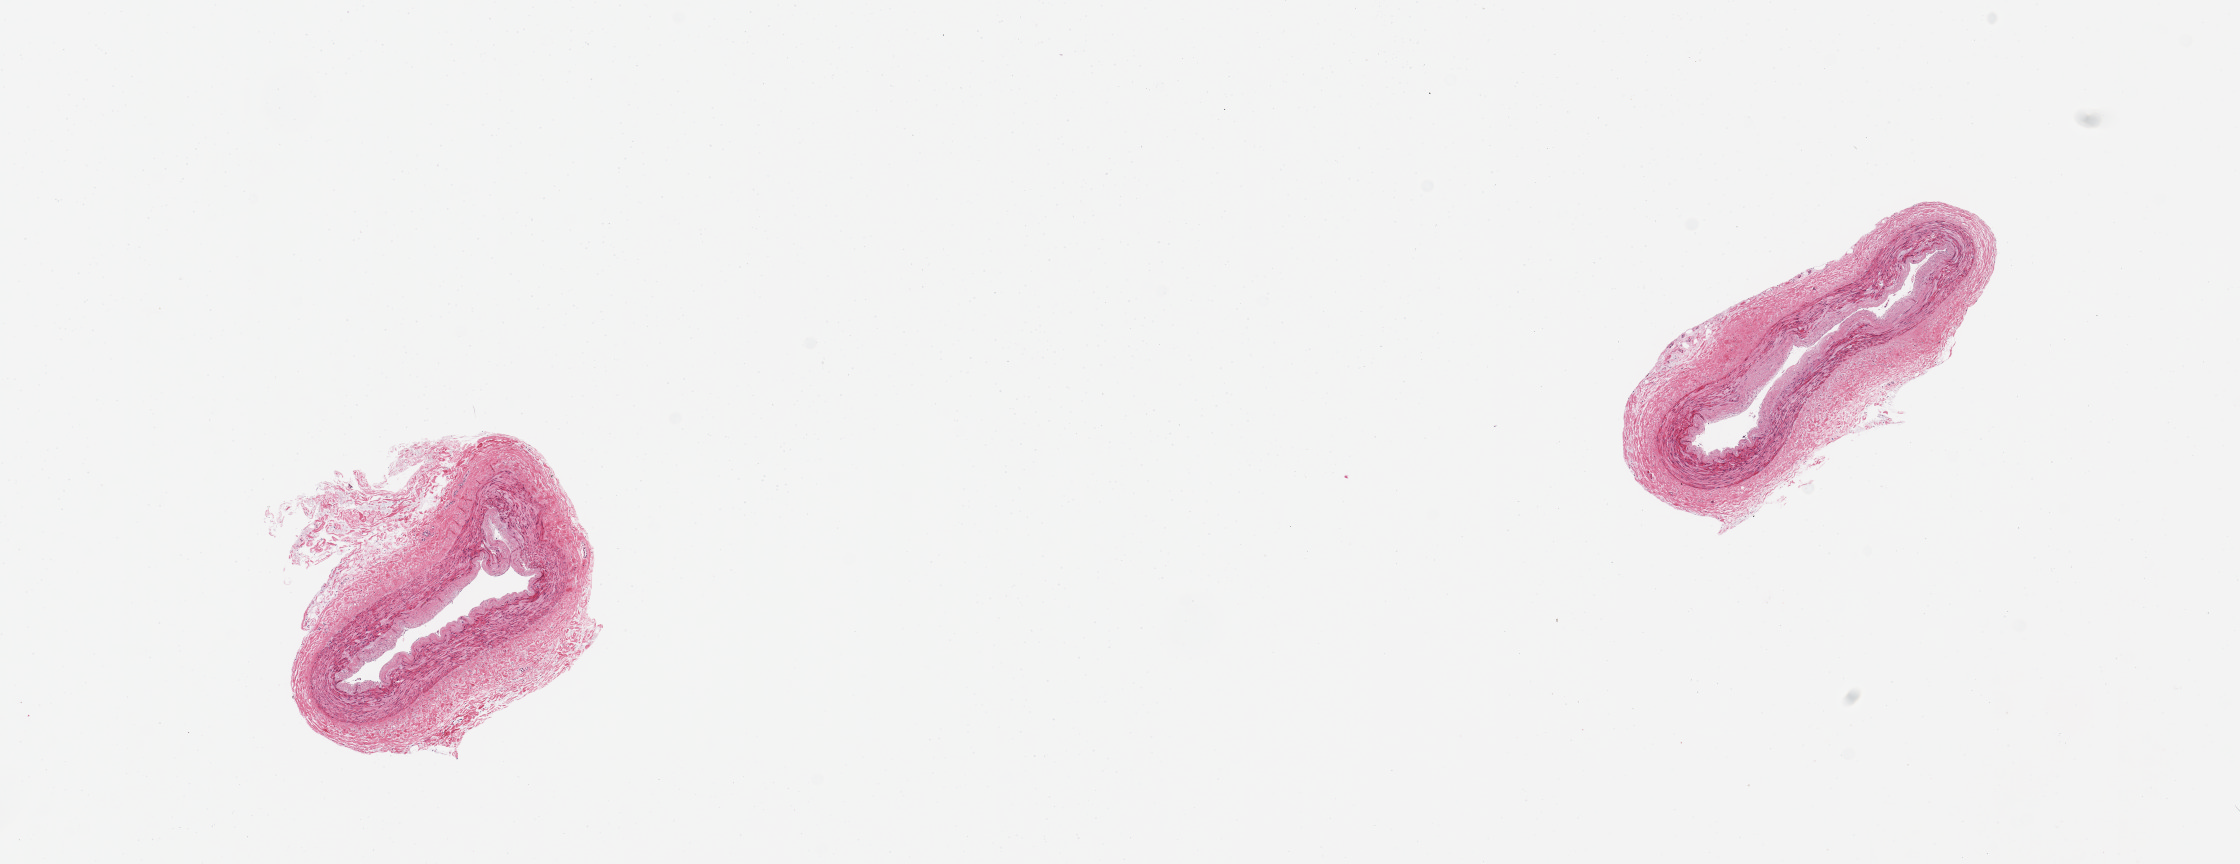
Digitized H&E-stained section — shown as a low-resolution overview of the whole scanned area (about 17.7 x 6.8 mm), PAXgene-fixed, paraffin-embedded tissue, target tissue: tibial artery, tissue donor sample. Donor: male.
Review note (as recorded): 2 pieces; mild plaque.